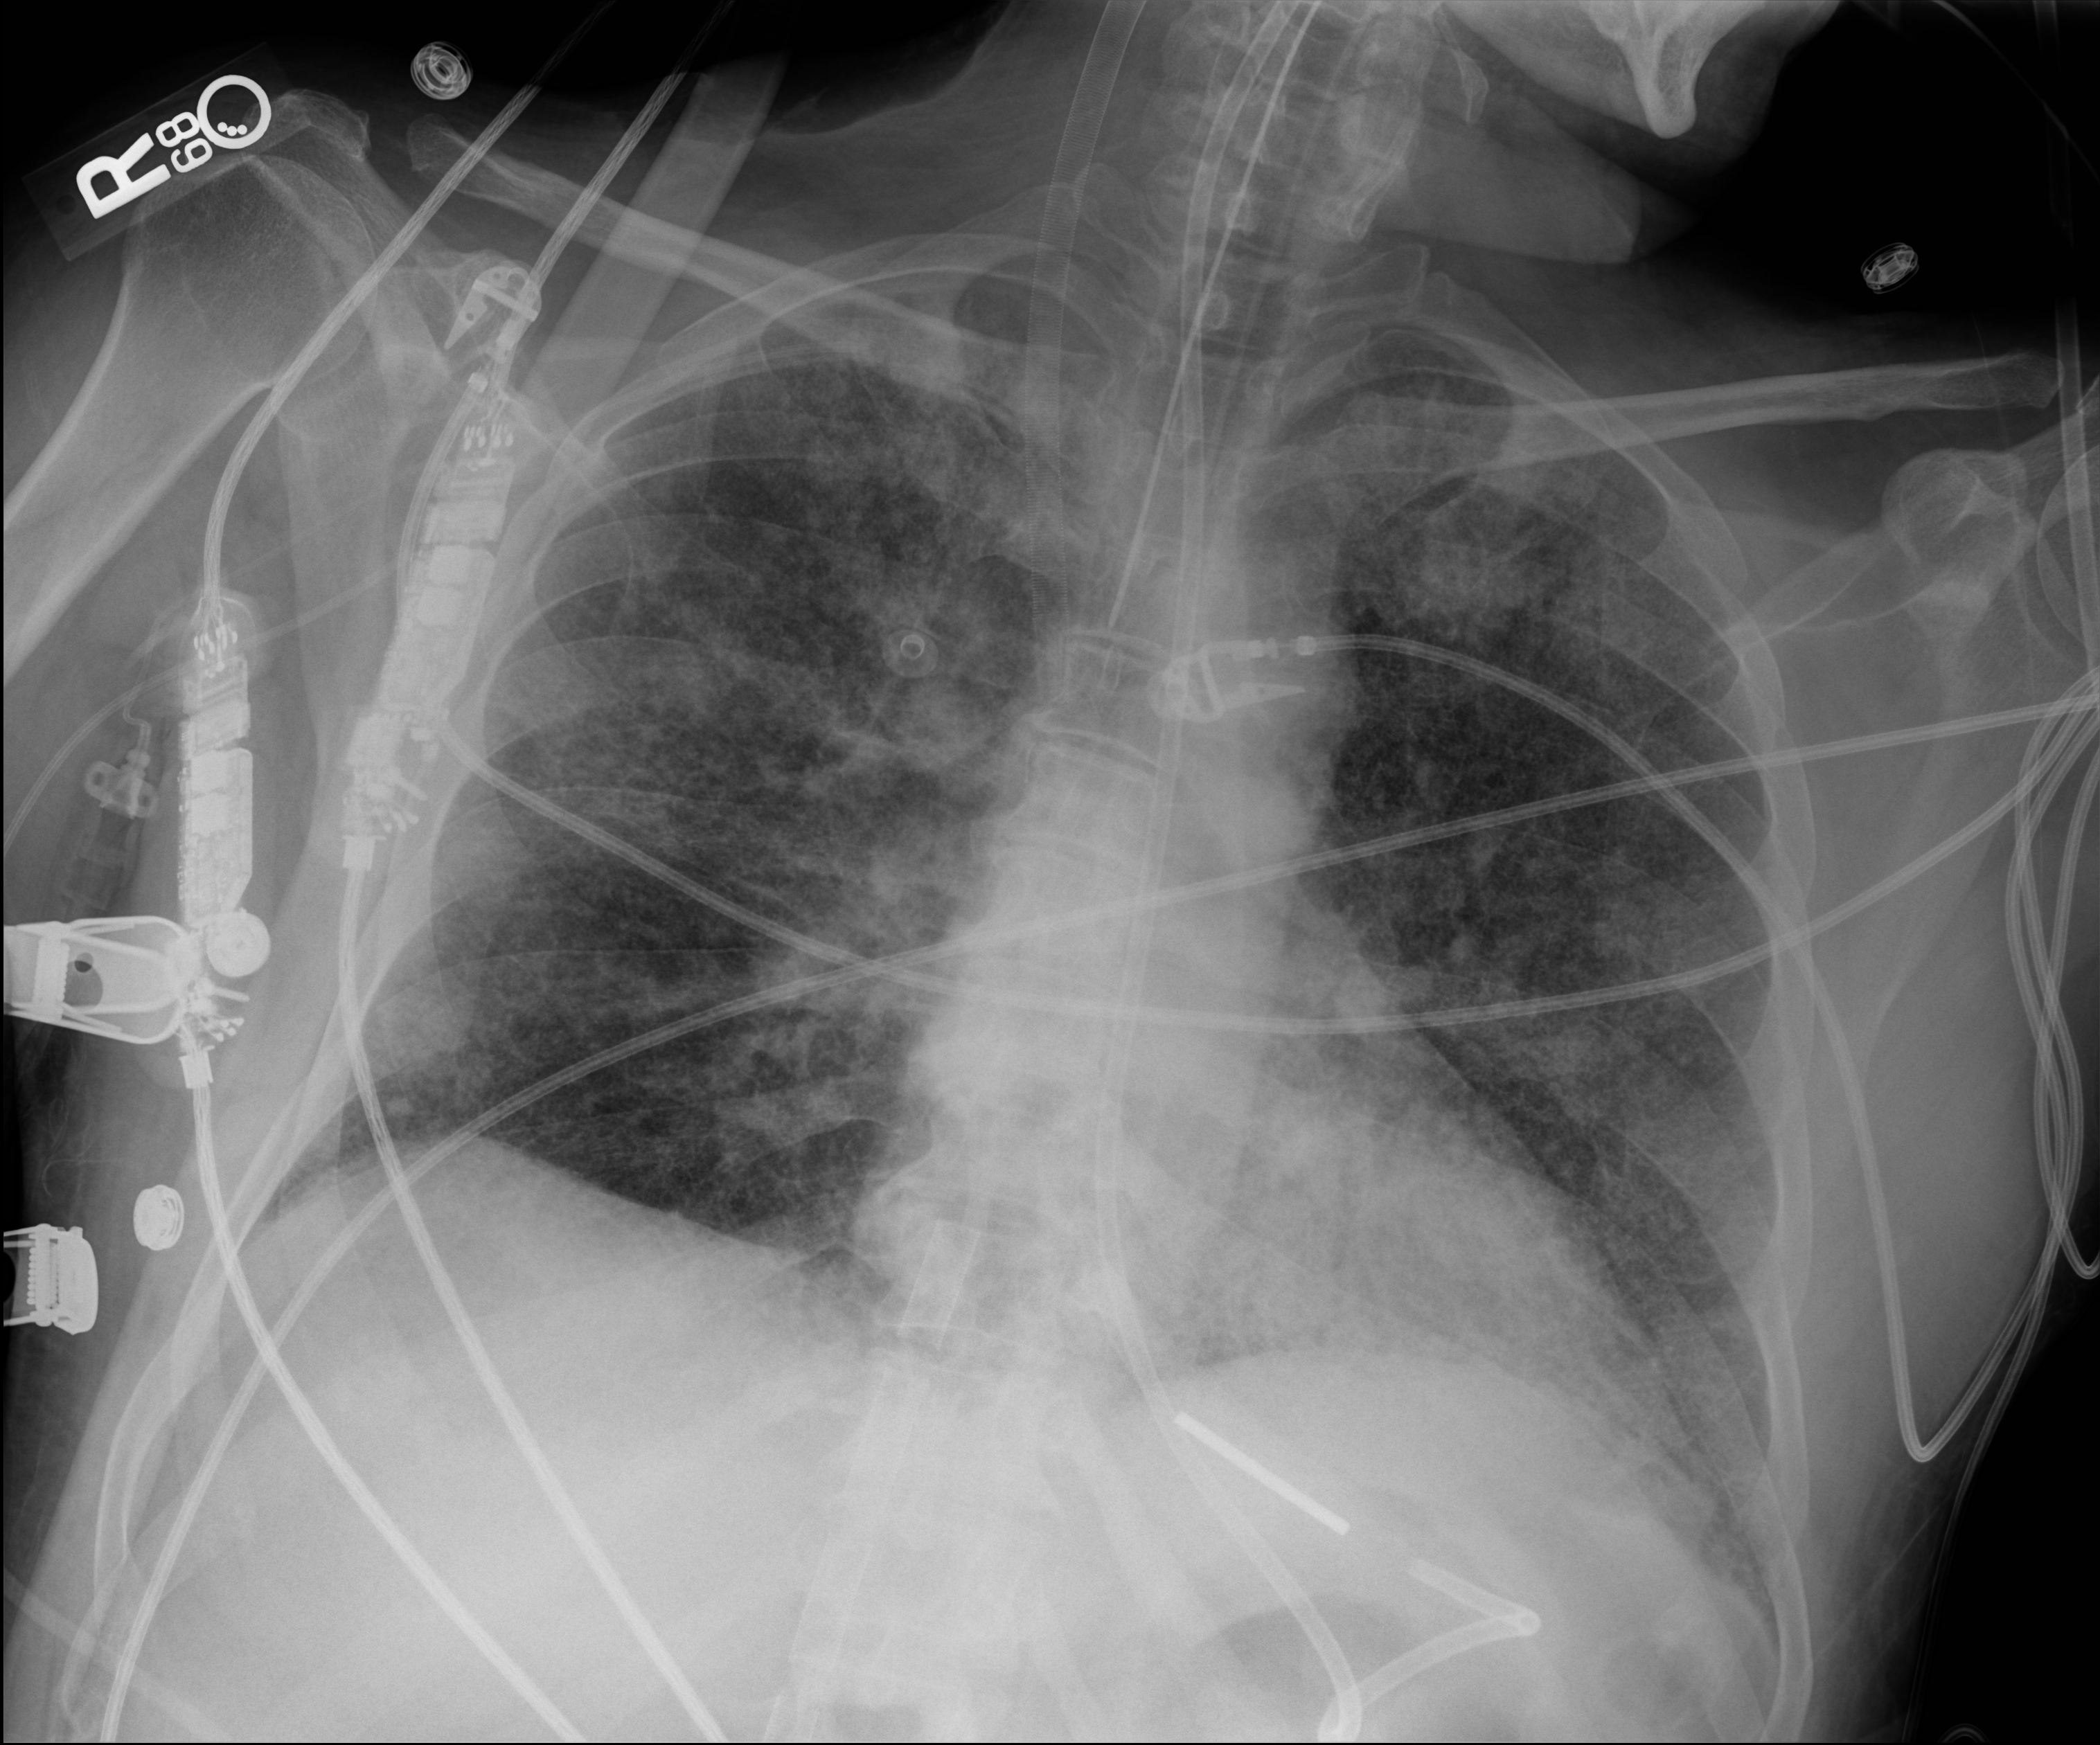
Chest radiograph; anteroposterior (AP) projection. Male patient hospitalised with COVID-19, age 18–59 years.
Hospital-stay facts (about this admission, not read from this image; timing relative to this image not recorded):
- admitted to intensive care during this hospital stay: yes